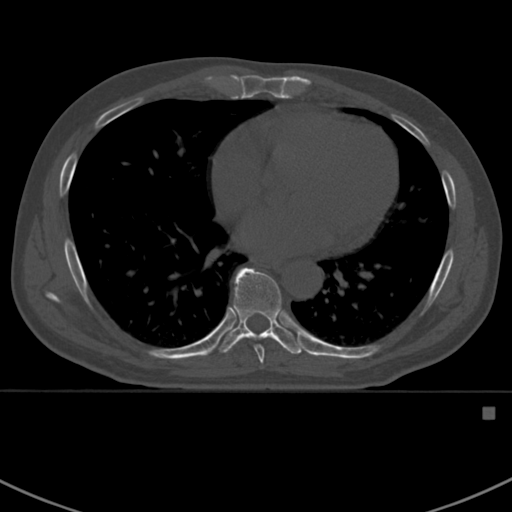
CT including the spine, one axial slice. Position 405 of 412 along the scan axis. Reconstruction kernel Br40s. 120 kVp. Bone window (W 1800 / L 400 HU). 1.5 mm slice thickness. 512 × 512 image matrix, field of view 358 × 358 mm. Patient: male, 59 years. From the clinical record (not read from this slice): primary cancer: prostate.
Structures marked on this image (semi-automatically segmented with operator editing):
- T7 vertebra: bounding box [x1, y1, x2, y2] px = [255, 345, 264, 365]
- T8 vertebra: [218, 268, 303, 355]